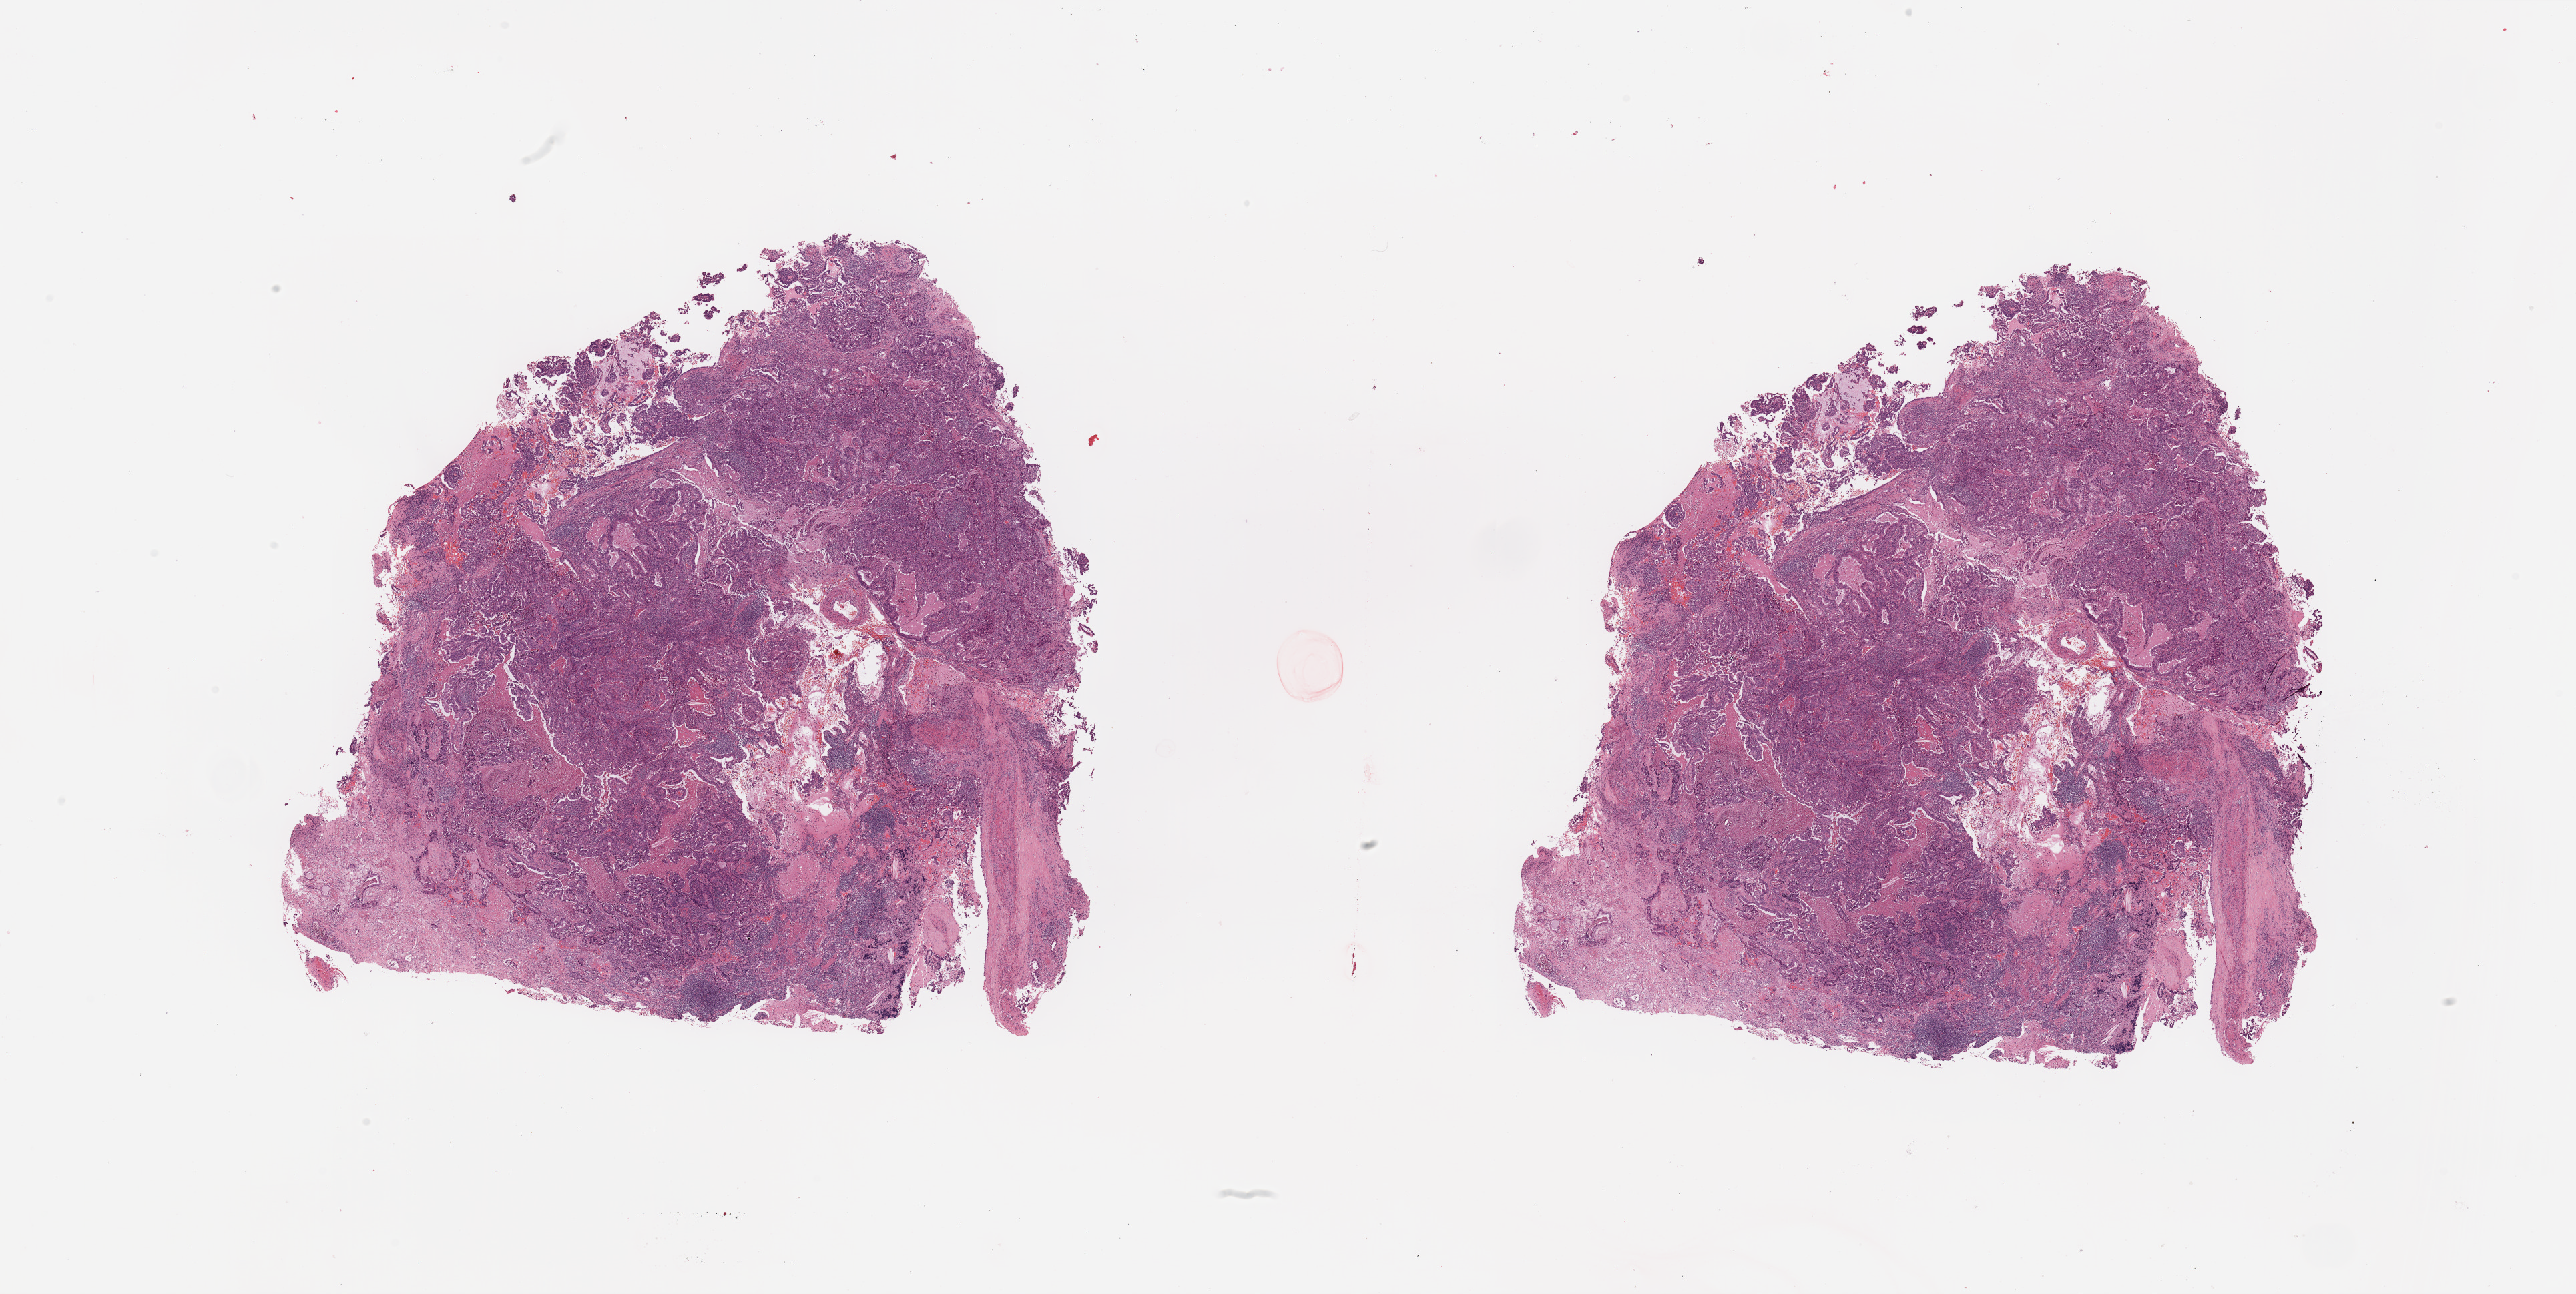
H&E whole-slide image, low-resolution overview of the scanned area, about 30.5 x 15.3 mm; tumour tissue sample, sampled site: lung. Male, 63 y/o.
Diagnosis: Adenocarcinoma, NOS.